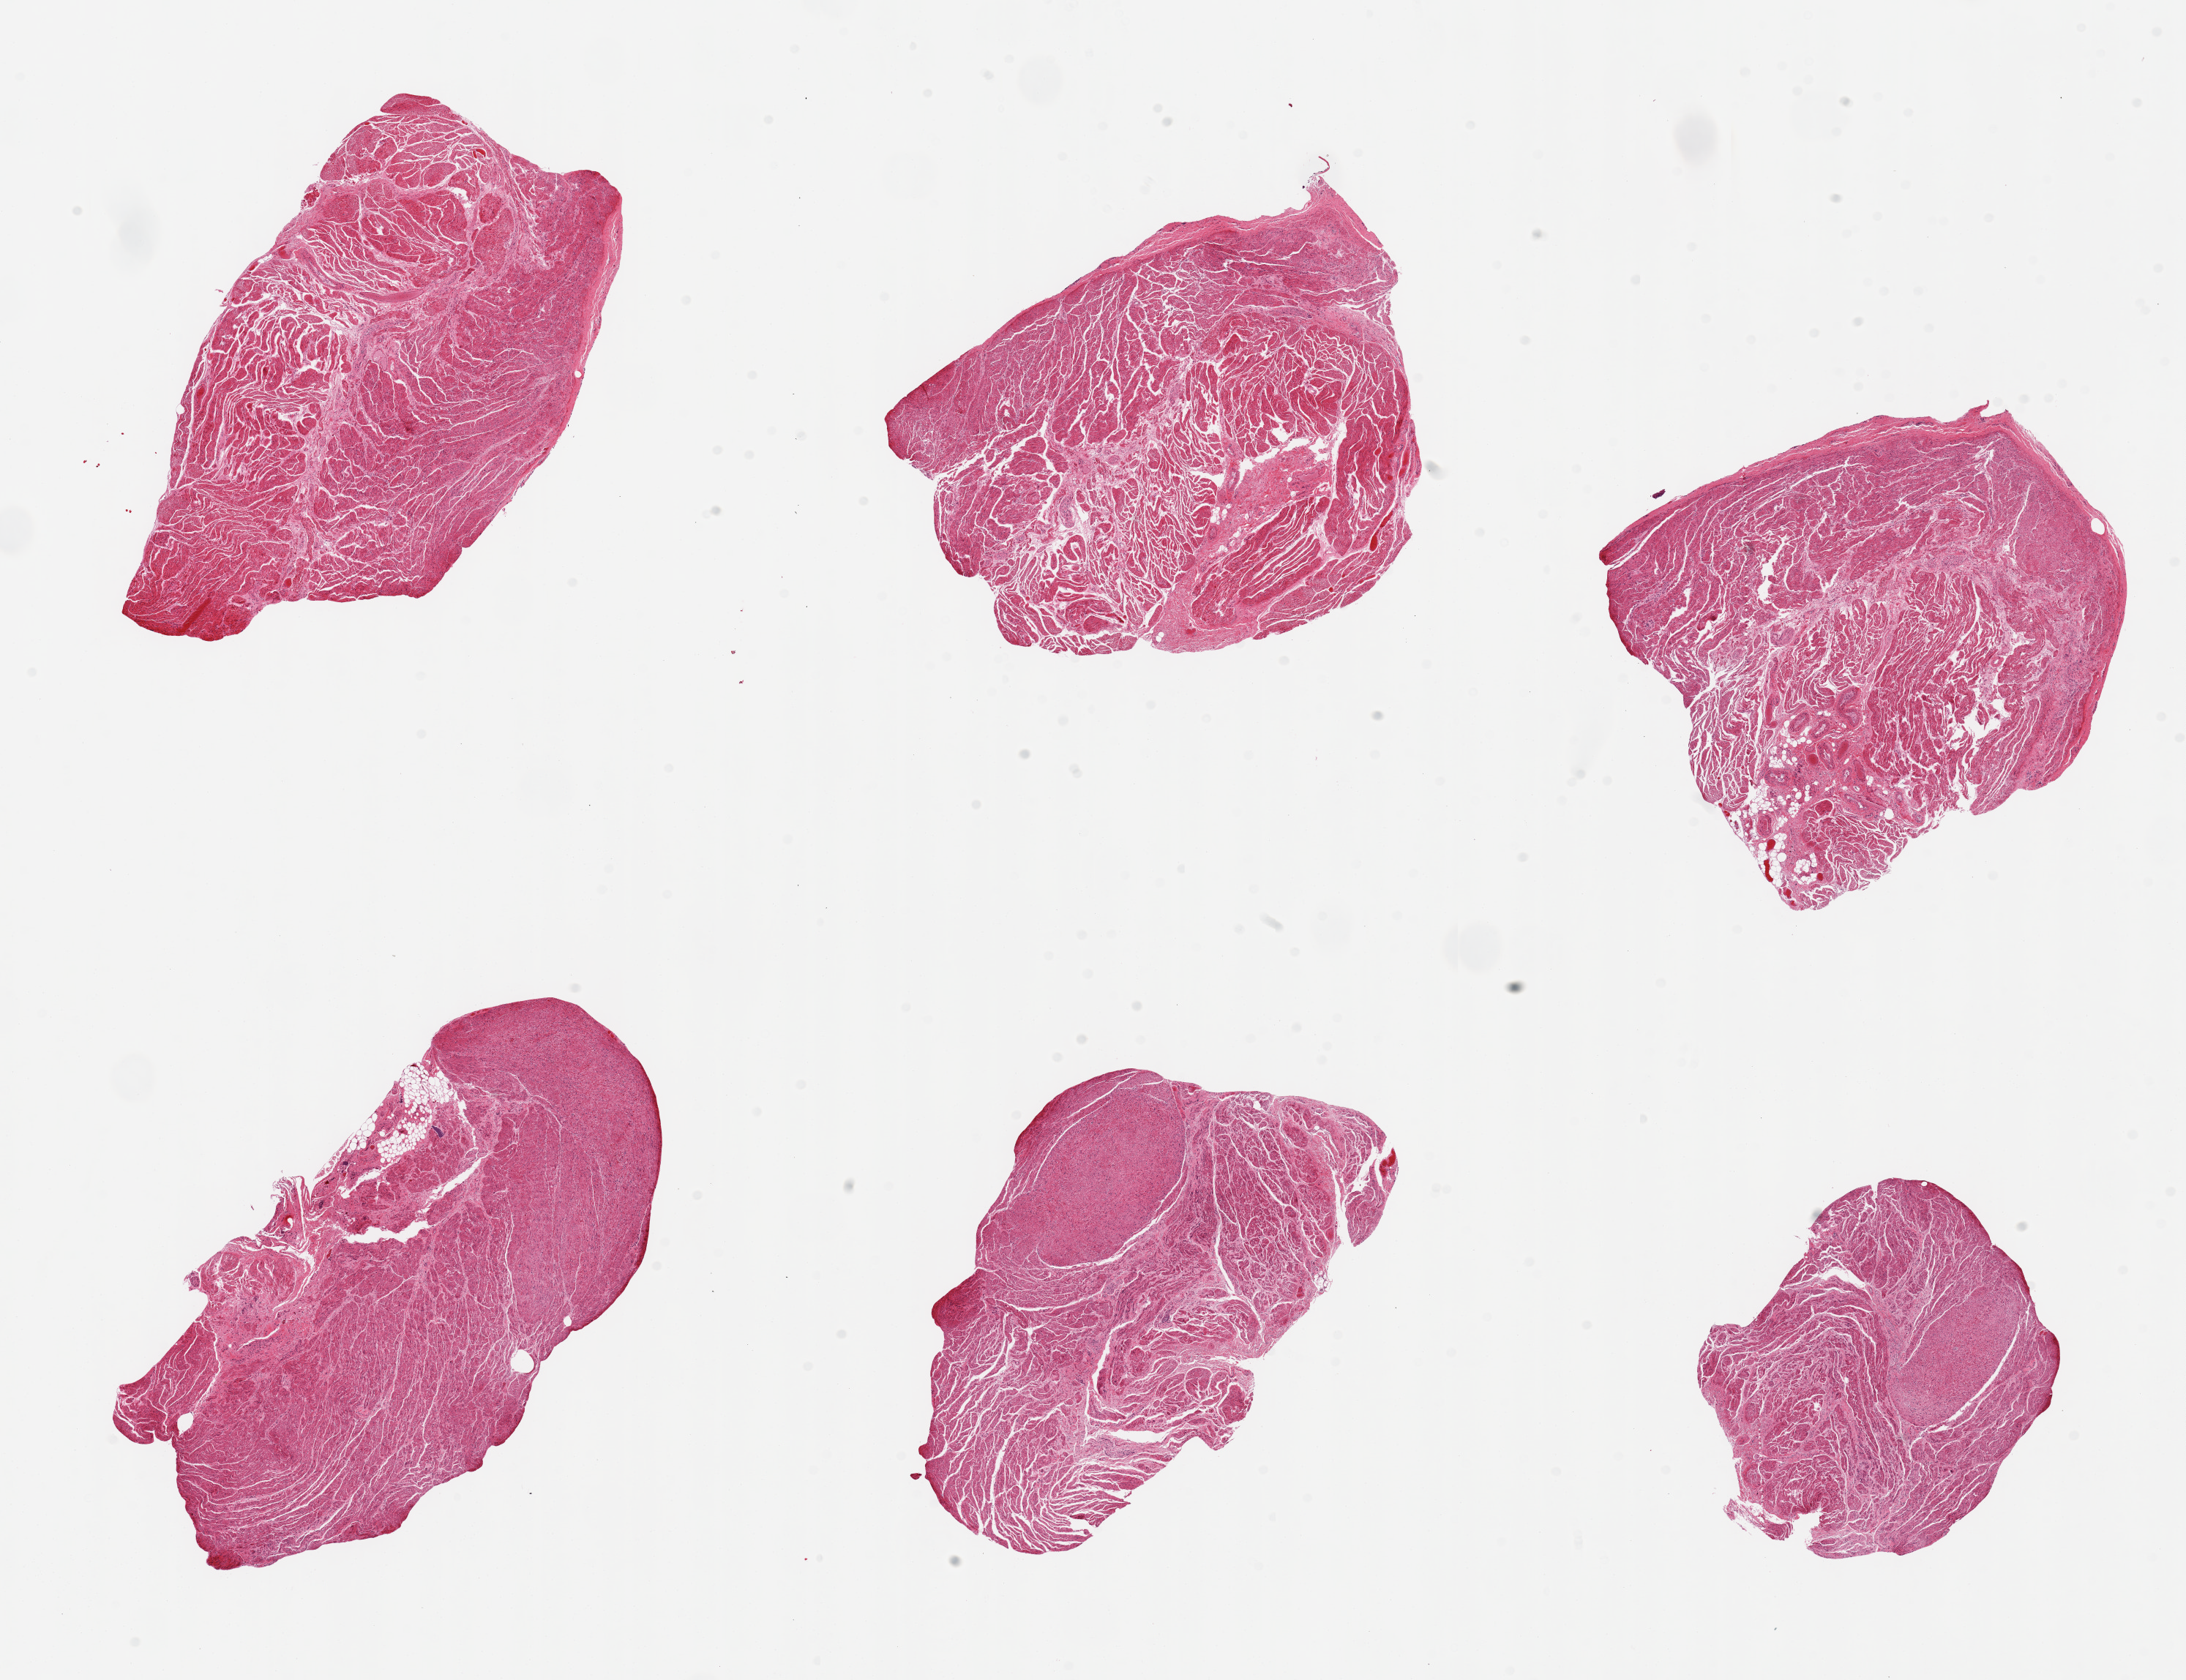
Whole-slide image, hematoxylin and eosin (H&E) stain, a low-resolution overview of the entire scanned area, about 23.6 x 18.2 mm (slide scanned at 20x); PAXgene-fixed paraffin-embedded (PFPE) section; section of gastroesophageal junction (target tissue); donor tissue sample.
Review note (as recorded): 6 pieces; well dissected.